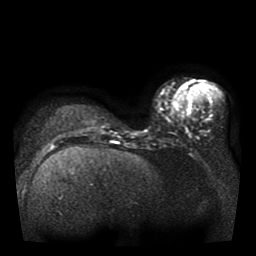
Breast MRI, one axial slice. Slice 16 of 41 in the series (ordered by position). Diffusion-weighted series; image 2 of 4 stored at this slice position (different b-values; order by instance number). 1.5 T. 5 mm slice thickness. 256 × 256 image matrix, field of view 330 × 330 mm. Female patient.
Outlined on this slice (manually delineated by an expert):
- tumour on diffusion-weighted imaging: box from (x=187, y=110) to (x=192, y=116) px